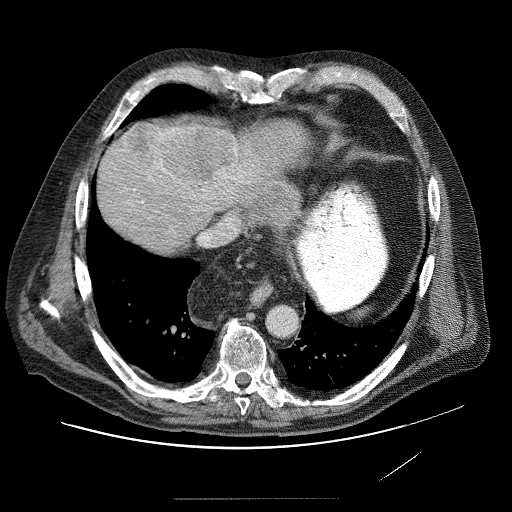
Contrast-enhanced abdominal CT (liver protocol), one axial slice; position 73 of 89 along the scan axis; soft-tissue window (W 400 / L 40 HU); 2.5 mm slice thickness; 512 × 512 image matrix, field of view 420 × 420 mm. Case-level facts recorded for this patient, not image findings: diagnosis: hepatocellular carcinoma (patient treated with transarterial chemoembolisation; whether this scan precedes or follows treatment is not stated here); TNM stage (as recorded): Stage-IVA; Child-Pugh class: A; tumour nodularity: multinodular.
Structures marked on this image (semi-automatic segmentation, software-assisted and operator-edited):
- liver parenchyma outside the tumour (the mass and vessels are separate outlines, so this box may not span the whole liver): bounding box <100,122,288,244> (left, top, right, bottom; pixels)
- mass: <127,120,297,215>
- liver vessels: <130,182,227,244>